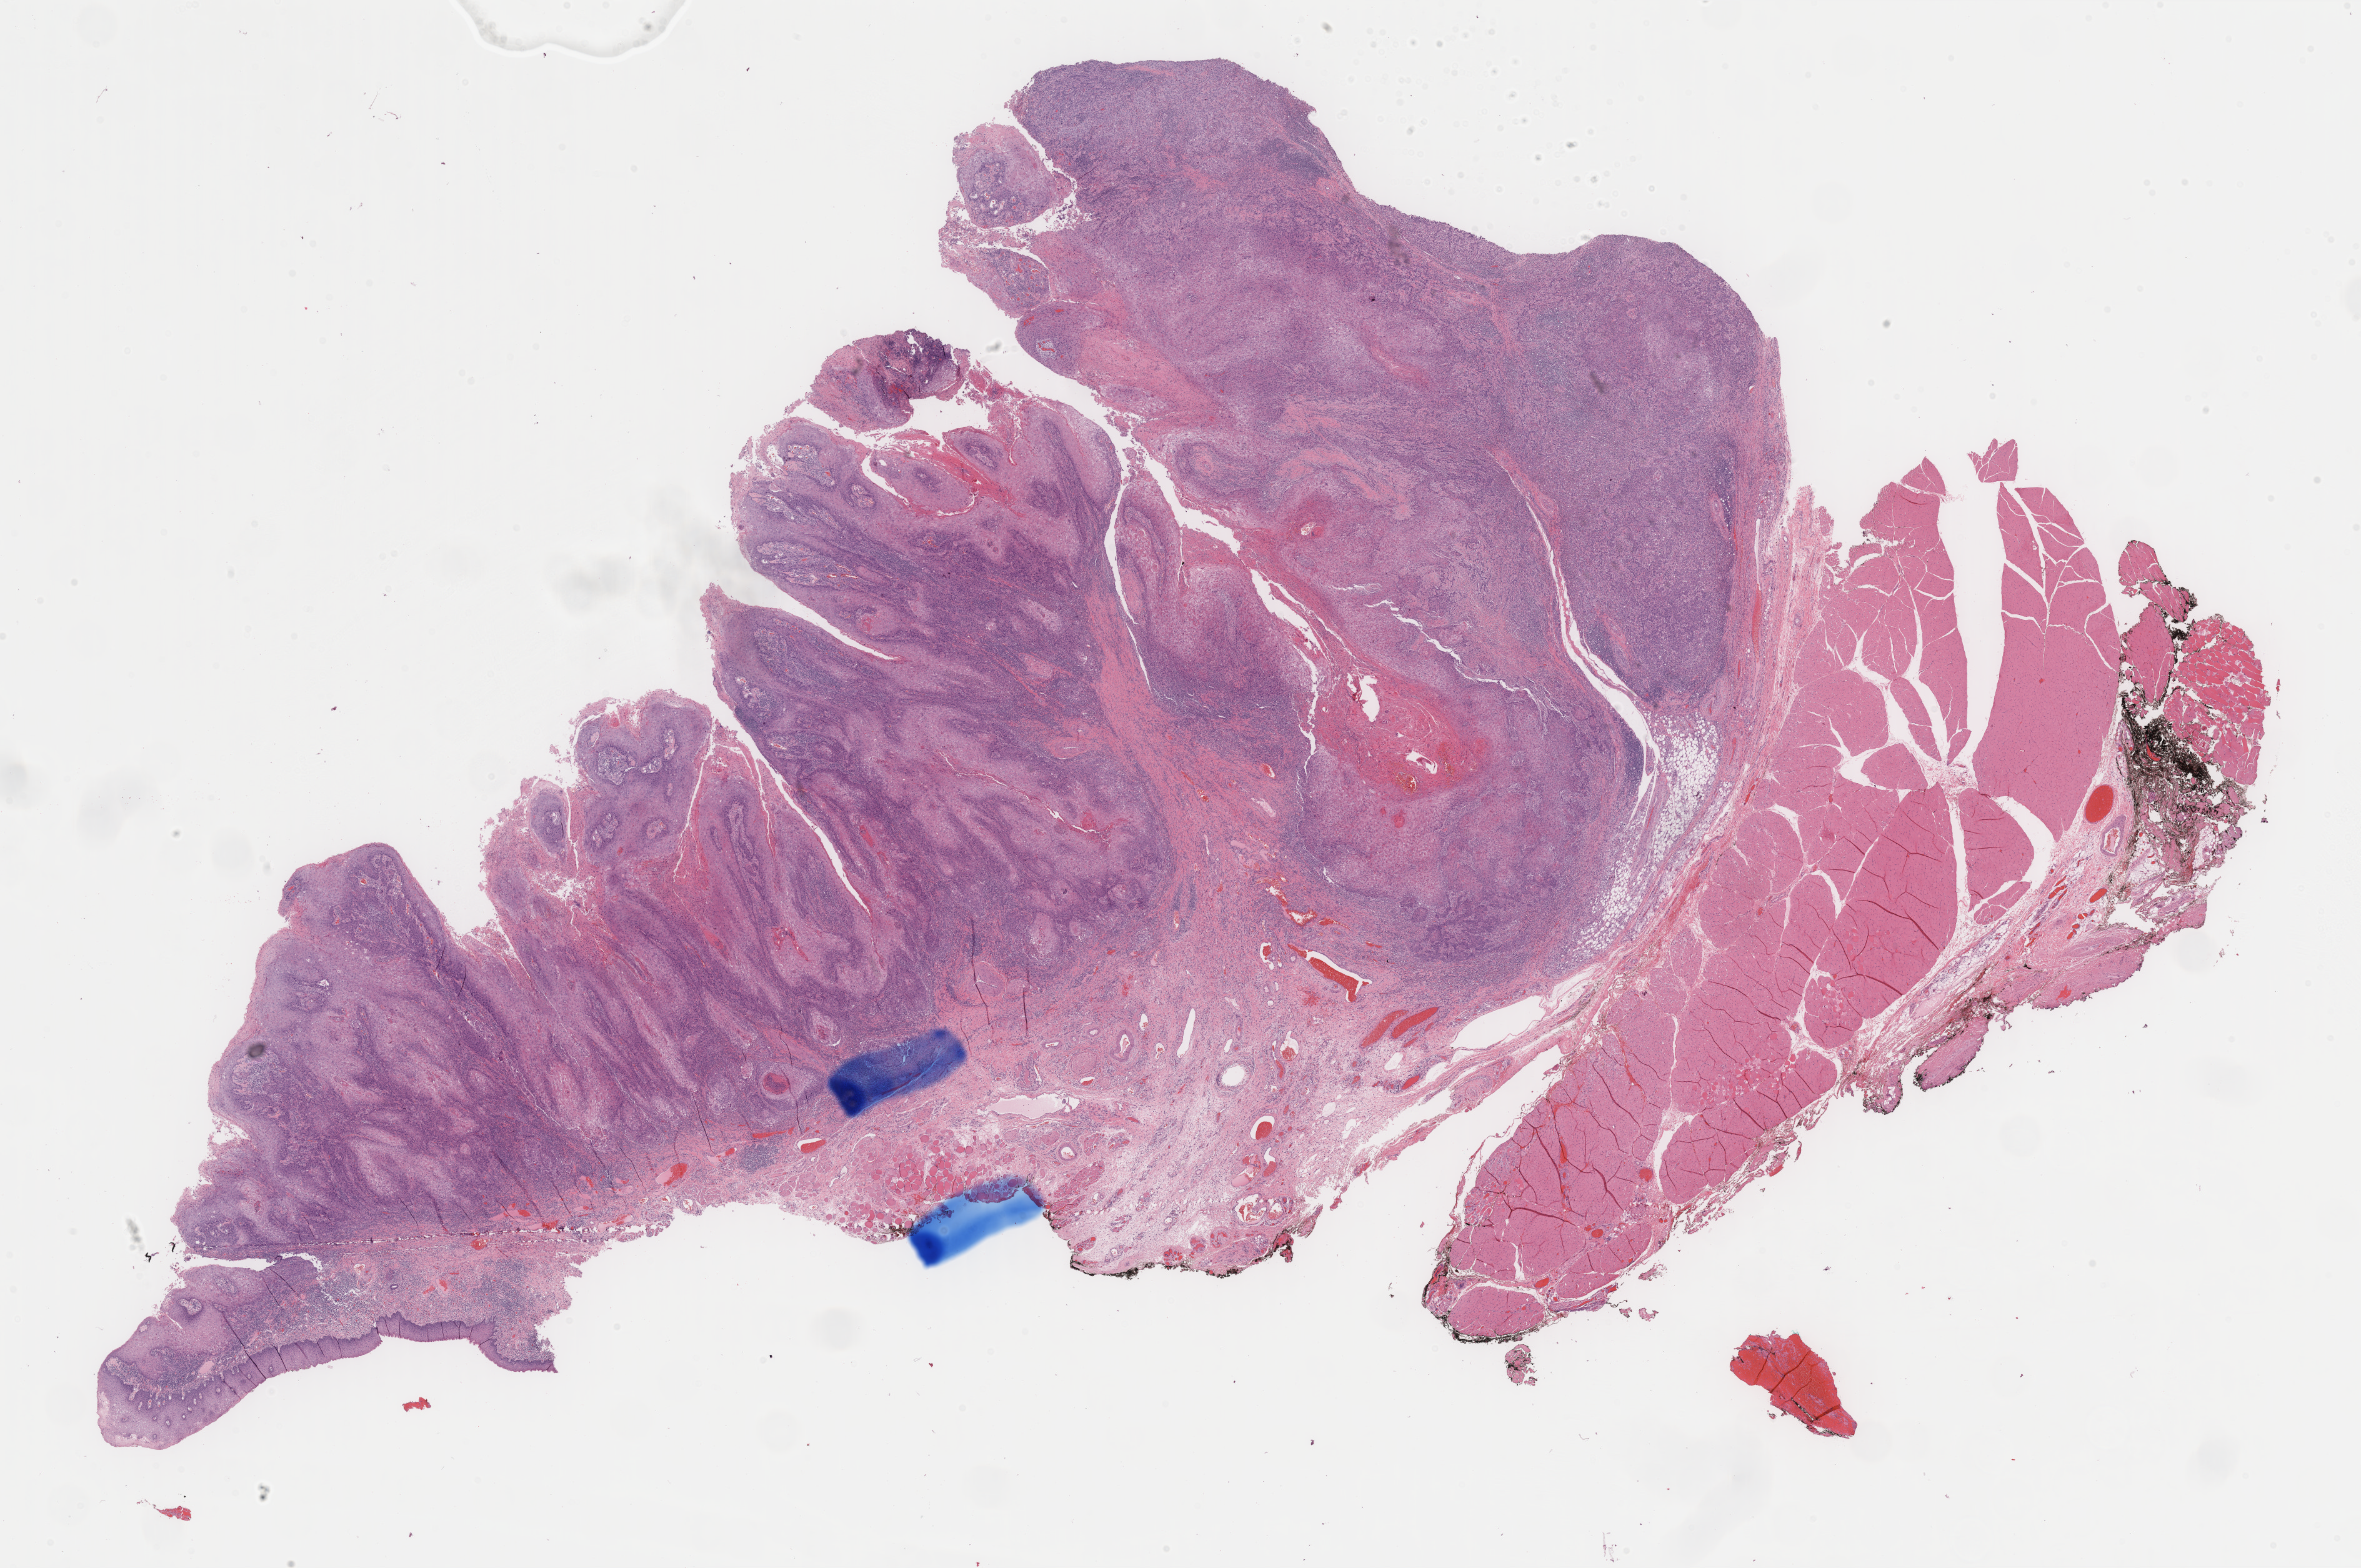
Whole-slide histology image, H&E-stained, shown as a low-resolution overview of the whole scanned area (about 29.9 x 19.8 mm, from a 40x scan). Formalin-fixed paraffin-embedded (FFPE) diagnostic section. Sample: primary tumour, head and neck. Female, age 41 years at initial diagnosis. Histologic grade: G2 (moderately differentiated).
TNM: T4a N2c M0. AJCC pathologic stage: IVA (7th edition). Pathologic diagnosis: Squamous cell carcinoma, NOS (supraglottis).